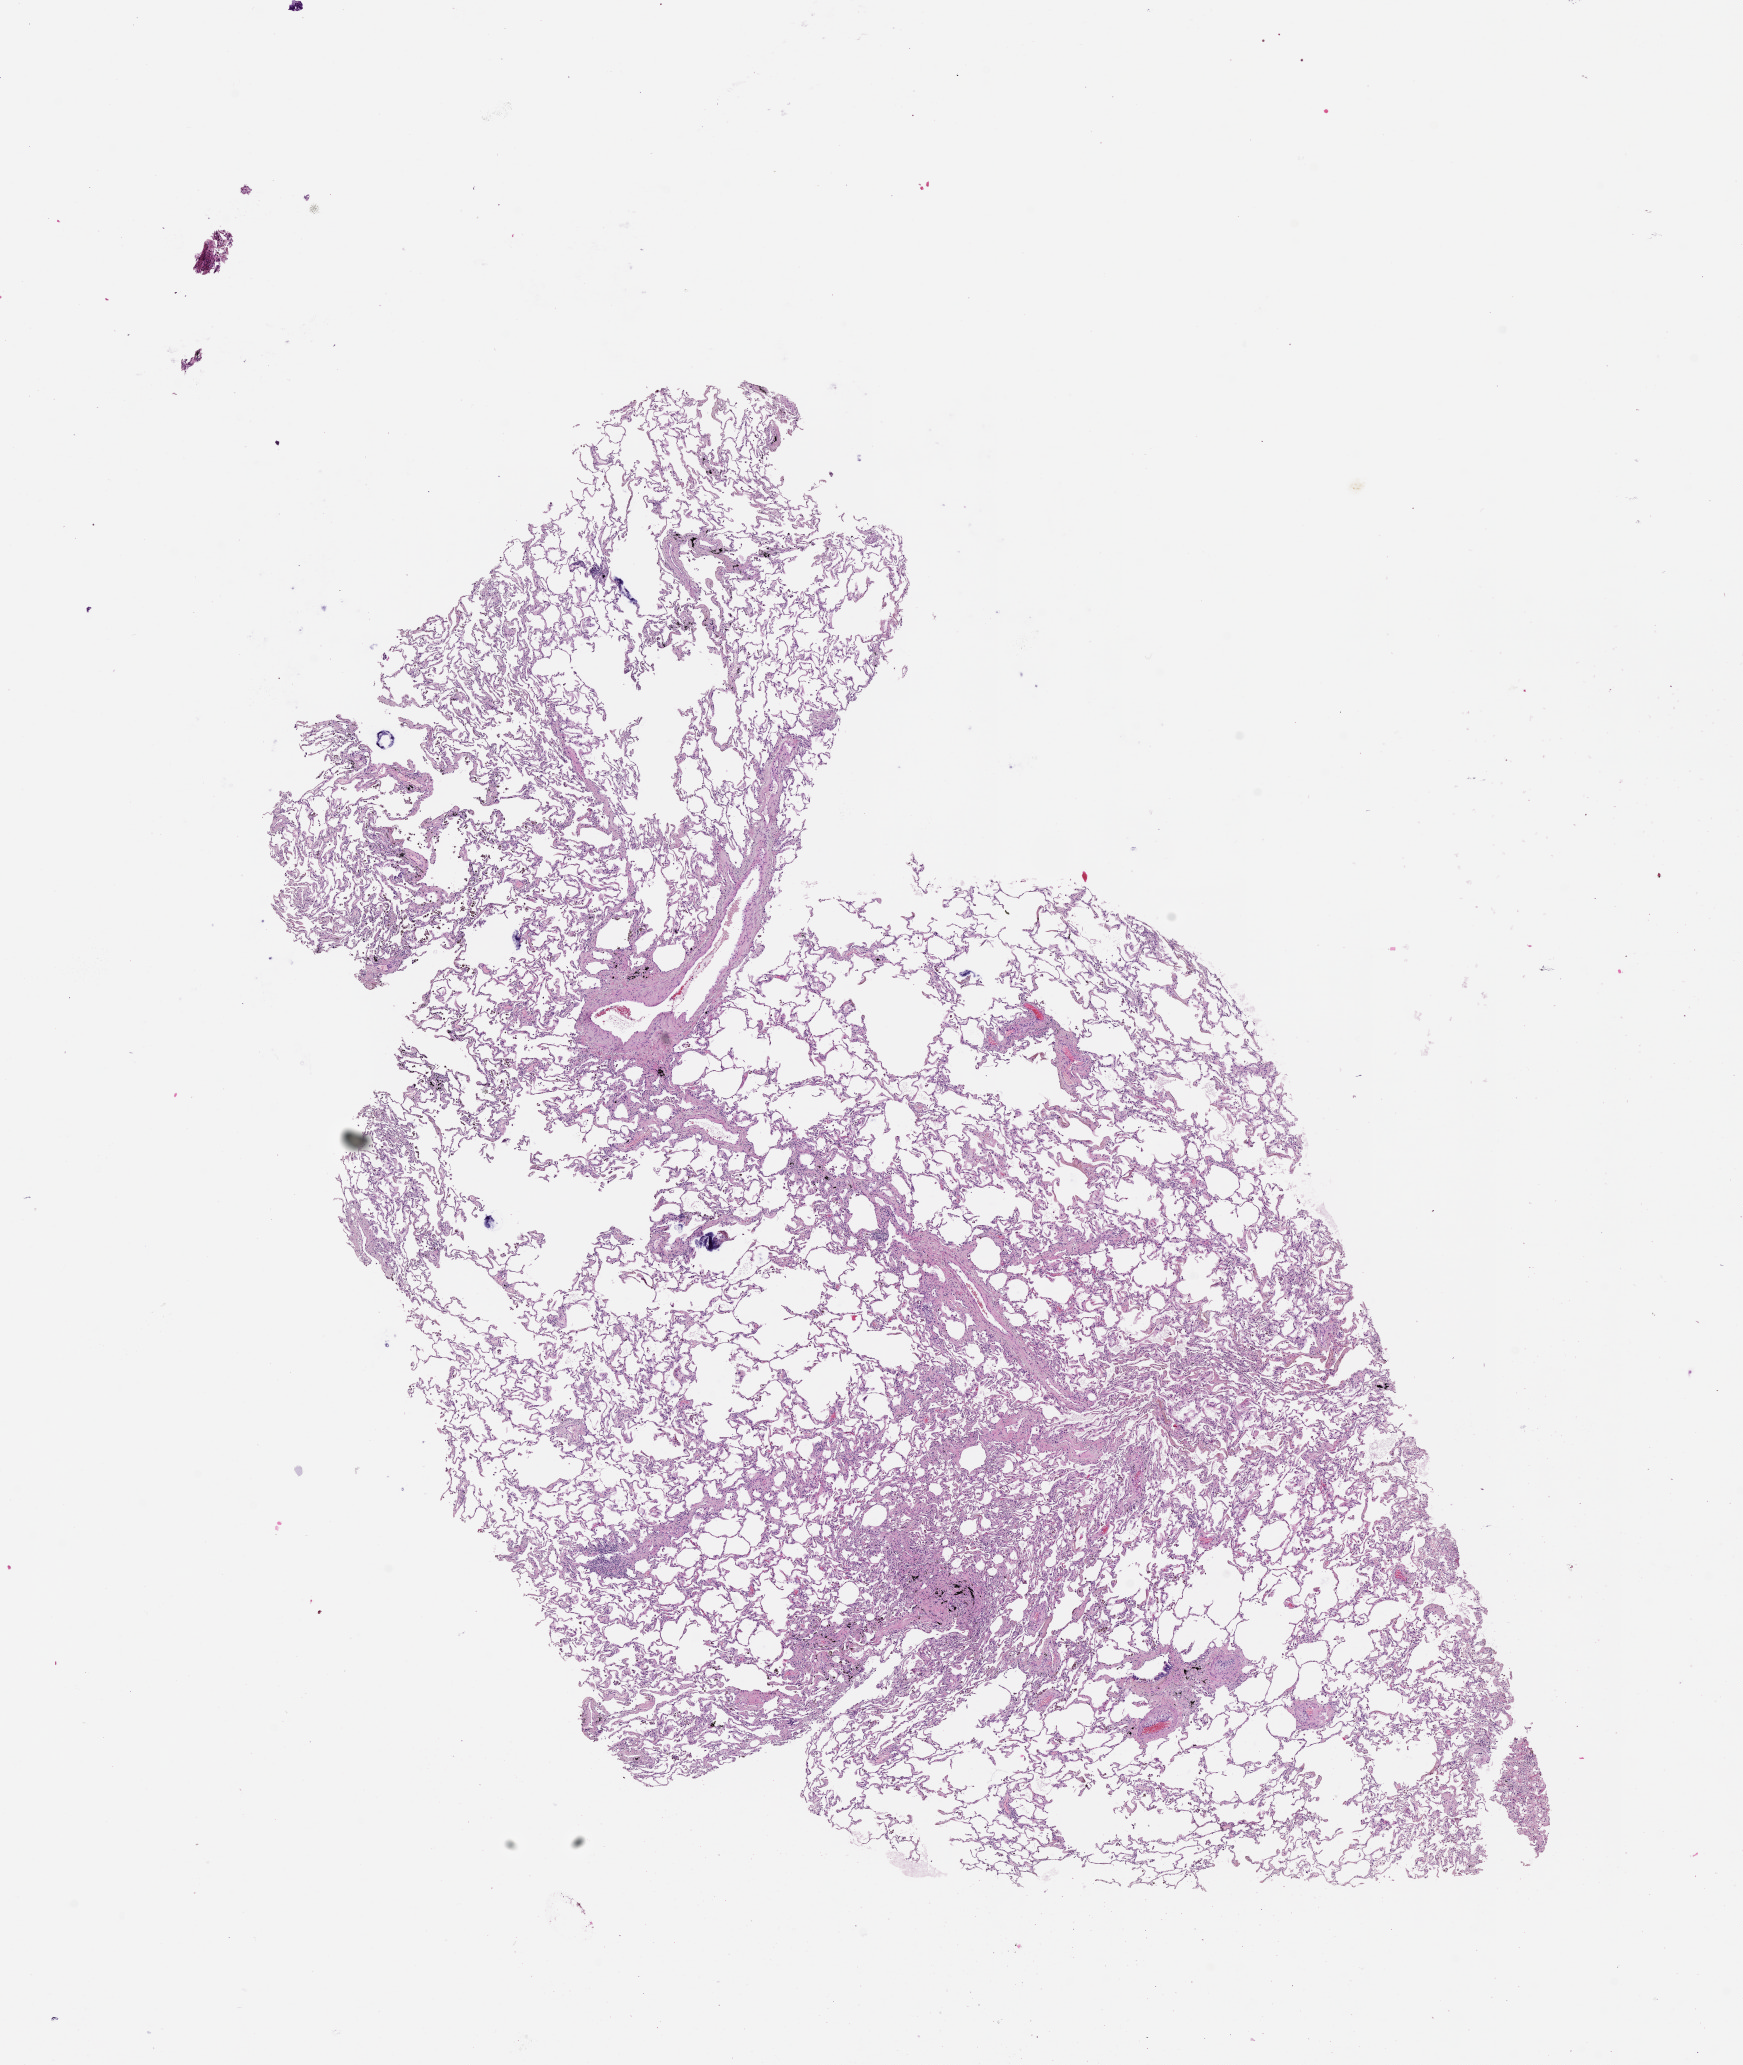
Hematoxylin and eosin (H&E) stained whole-slide image — low-resolution overview of the scanned area, about 14.0 x 16.6 mm (acquisition: 20x scan), lung, normal (non-tumour) tissue. Male, 60 y/o.
This section: normal (non-tumour) tissue from the same patient. Patient diagnosis (cohort enrolment): squamous cell carcinoma (lung).